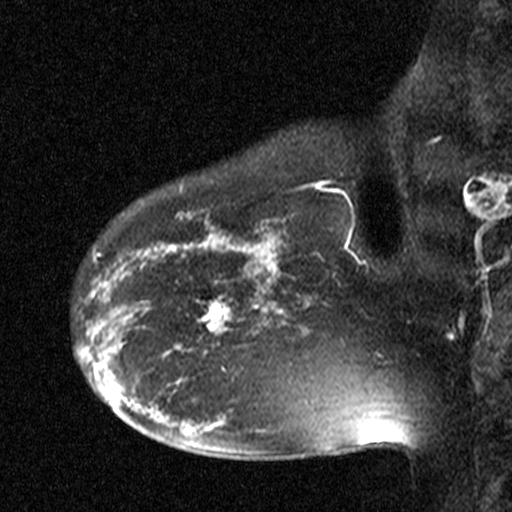
Breast MRI (dynamic contrast-enhanced), one sagittal slice; position 33 of 44 along the scan axis; dynamic contrast-enhanced study with each time point stored as its own series, time point 2 of 3 at this slice position (early post-contrast, ordered by acquisition time); 1.5 T; TE 4.5 ms, TR 11 ms; 3 mm slice thickness; 512 × 512 image matrix, field of view 200 × 200 mm. Female patient, age 38 years. From the clinical record (not read from this slice): setting: breast cancer imaged before/during neoadjuvant chemotherapy; receptor status: HR-positive, HER2-negative.
Outlined on this slice (semi-automatically segmented with operator editing):
- analysis volume of interest (the breast-tissue region the enhancement analysis was run in; not a lesion): bounding box <176,272,251,349> (left, top, right, bottom; pixels)
- tumour enhancement mask (voxels above the 90 % enhancement threshold inside the analysis volume of interest): <176,297,231,348>